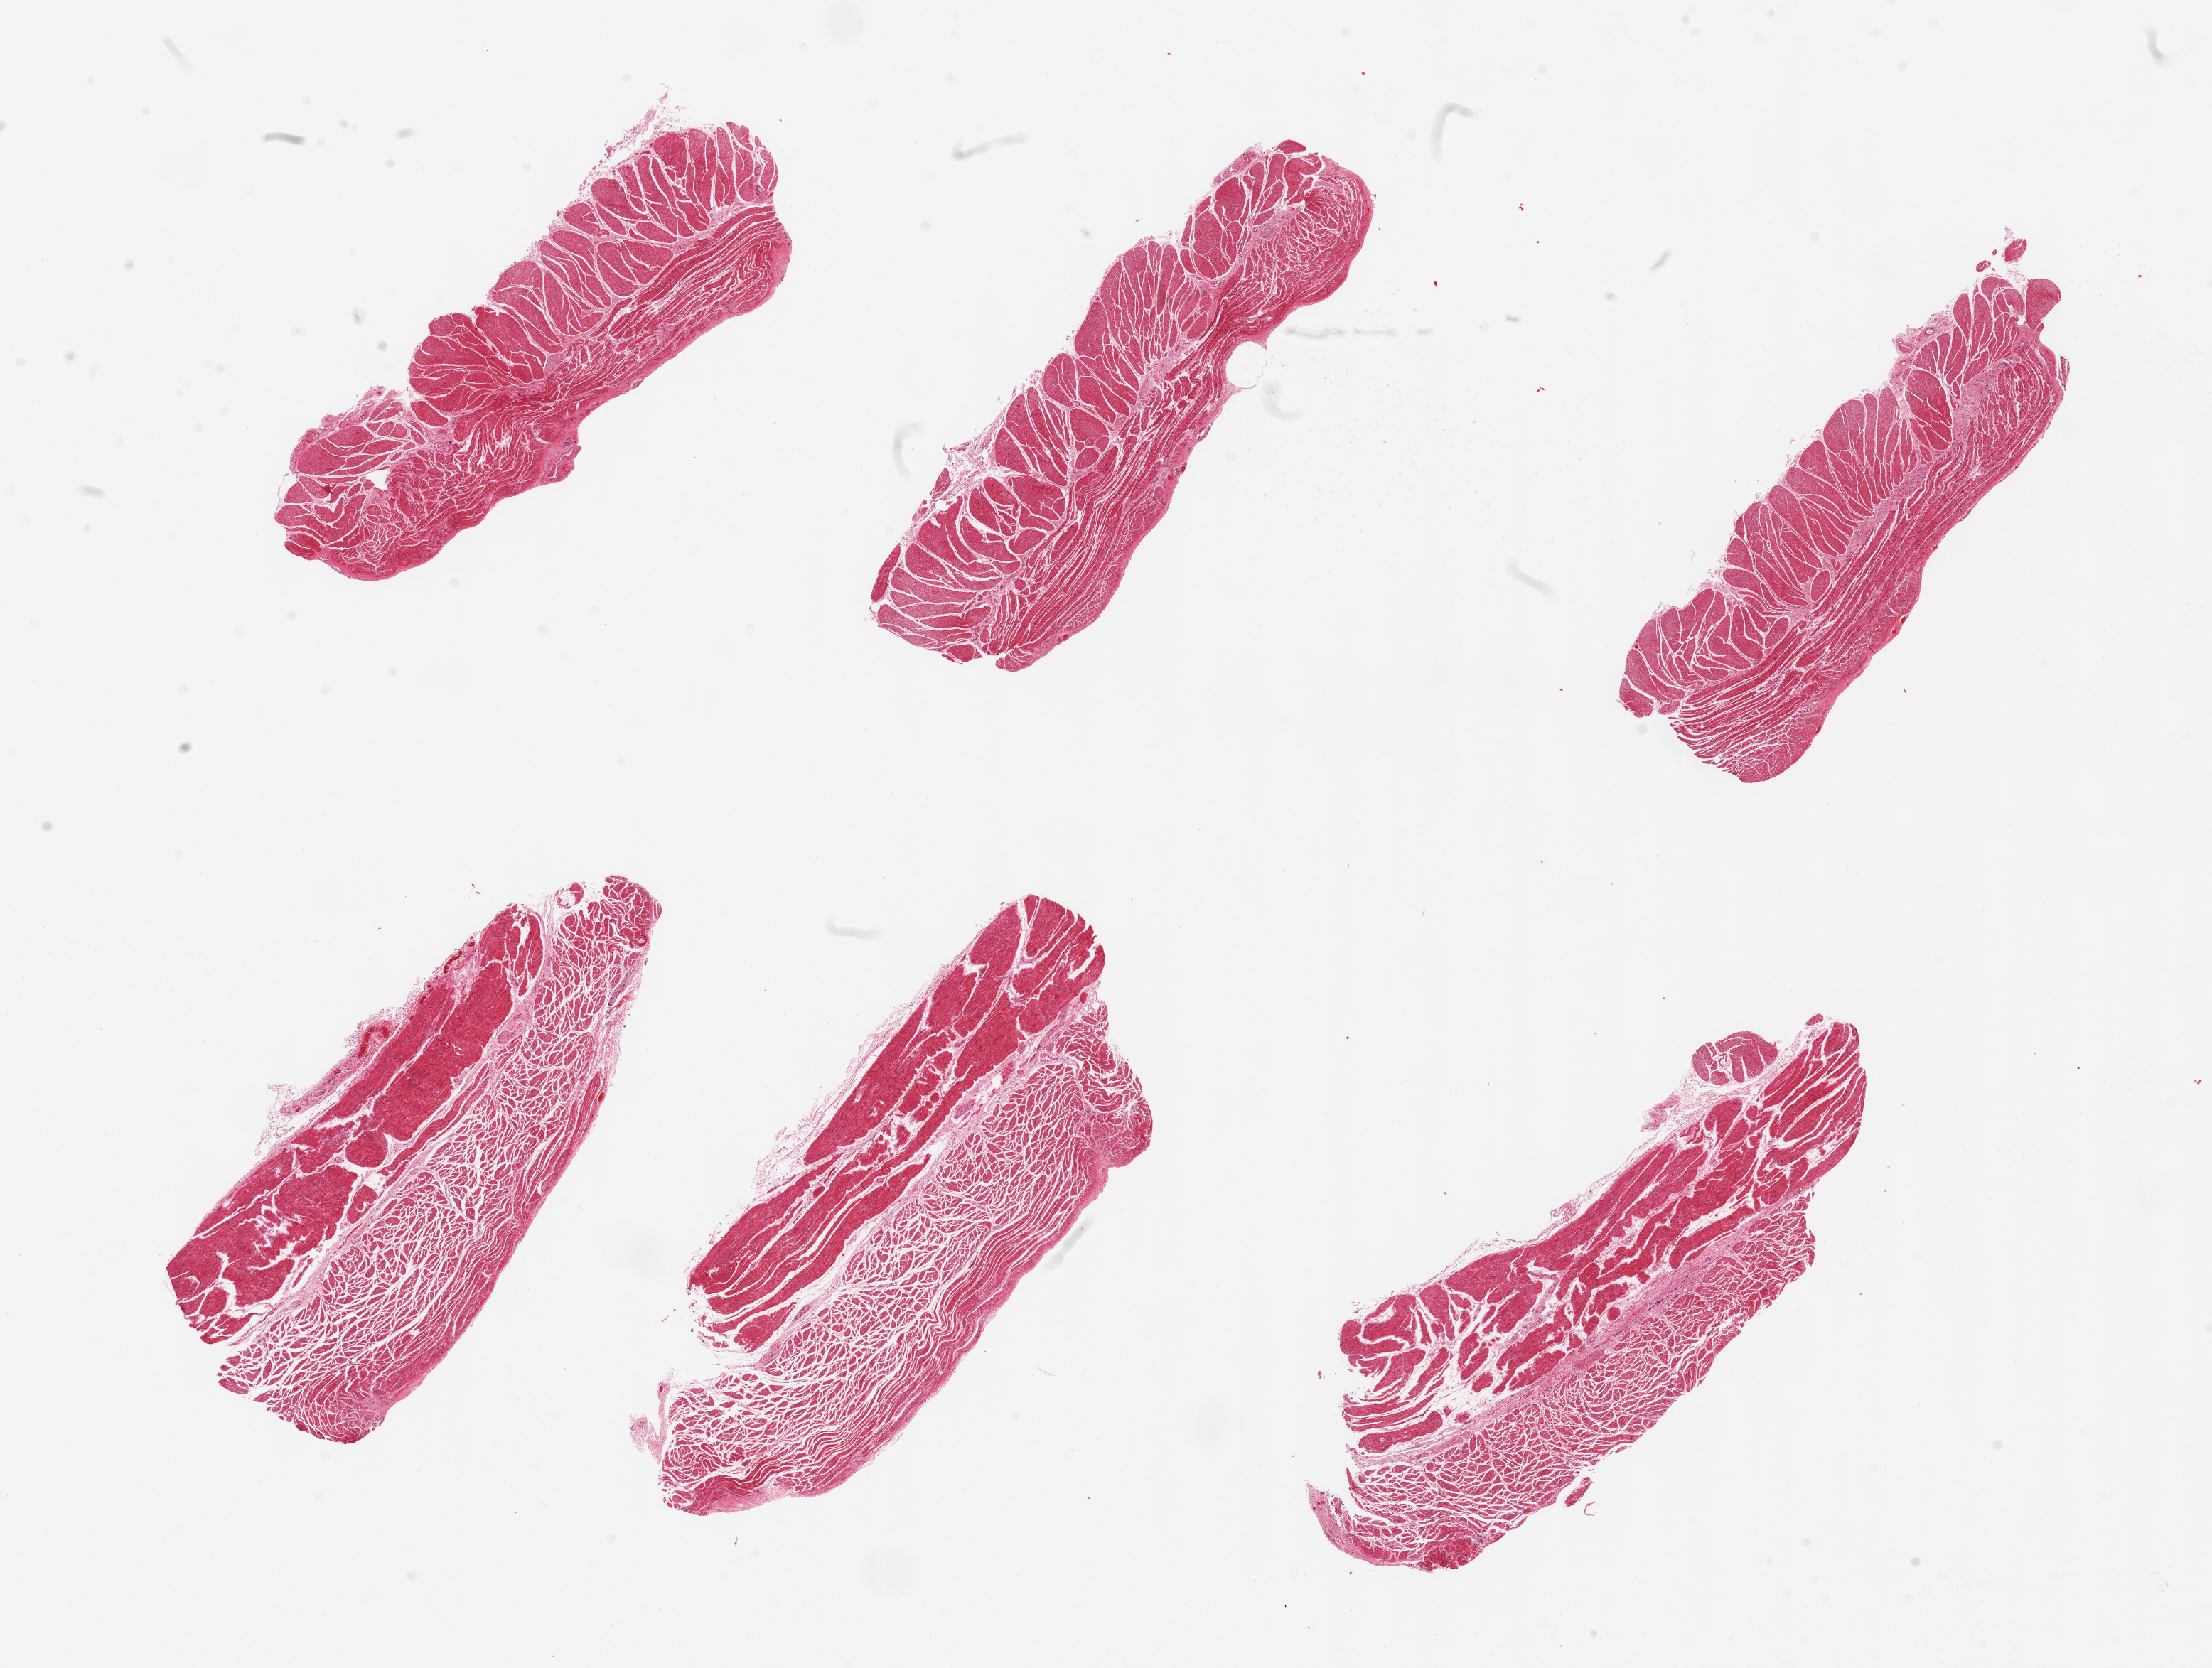
H&E whole-slide image — low-resolution overview of the scanned area, about 24.6 x 18.6 mm. PAXgene-fixed, paraffin-embedded tissue. Sampled site (target tissue): esophageal muscle. Tissue donor sample. Donor sex: male.
Reviewer comment on this tissue sample: 6 pieces, all muscularis.